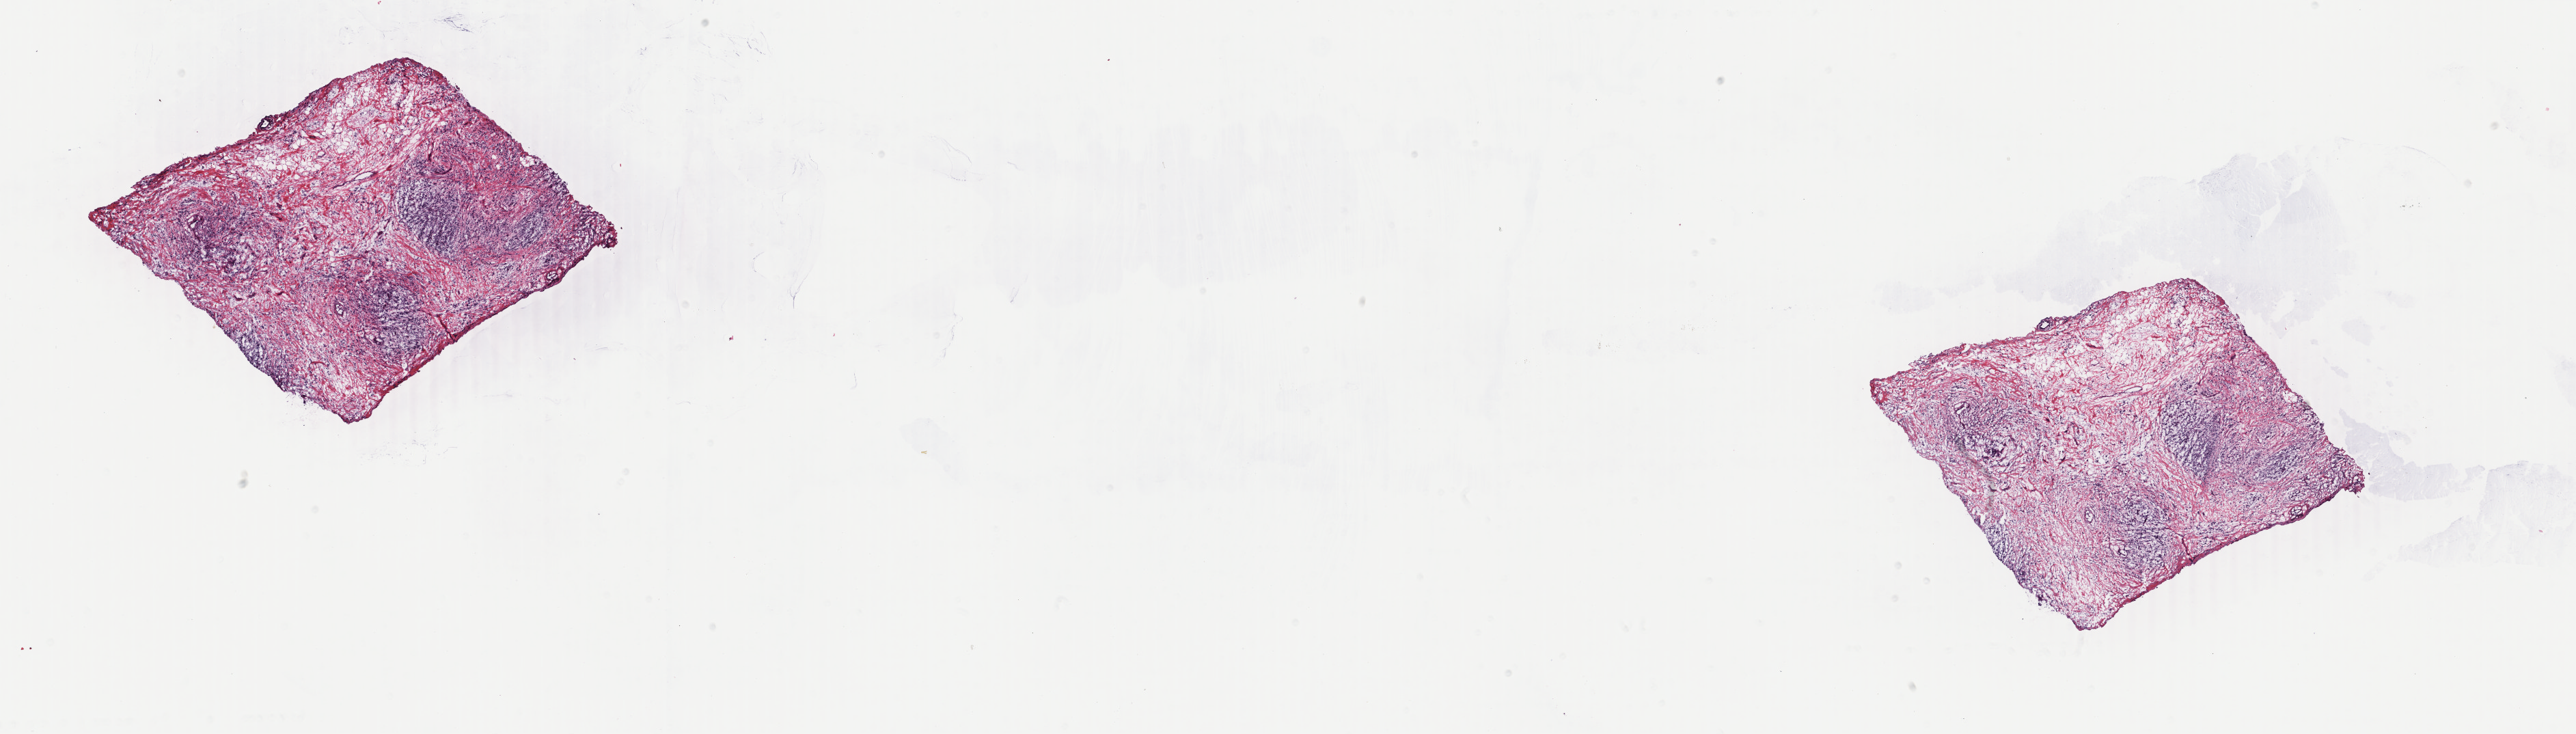
Digitized Hematoxylin and eosin (H&E) stained tissue section (whole slide), shown as a low-resolution overview of the whole scanned area (about 30.0 x 8.5 mm), frozen section, sample: primary tumour, breast. Female, age 38 years at initial diagnosis. Composition of this section per pathologist review: tumour cells 70%, tumour nuclei 70%, normal cells 0%, stromal cells 28%, necrosis 2%. Inflammatory infiltration, as recorded: lymphocyte infiltration 2%, monocyte infiltration 0%, neutrophil infiltration 0%.
* TNM: T3 N1b M0
* AJCC pathologic stage: IIIA
* lymph nodes positive (case pathology): 6 of 24 examined
* diagnosis: Lobular carcinoma, NOS